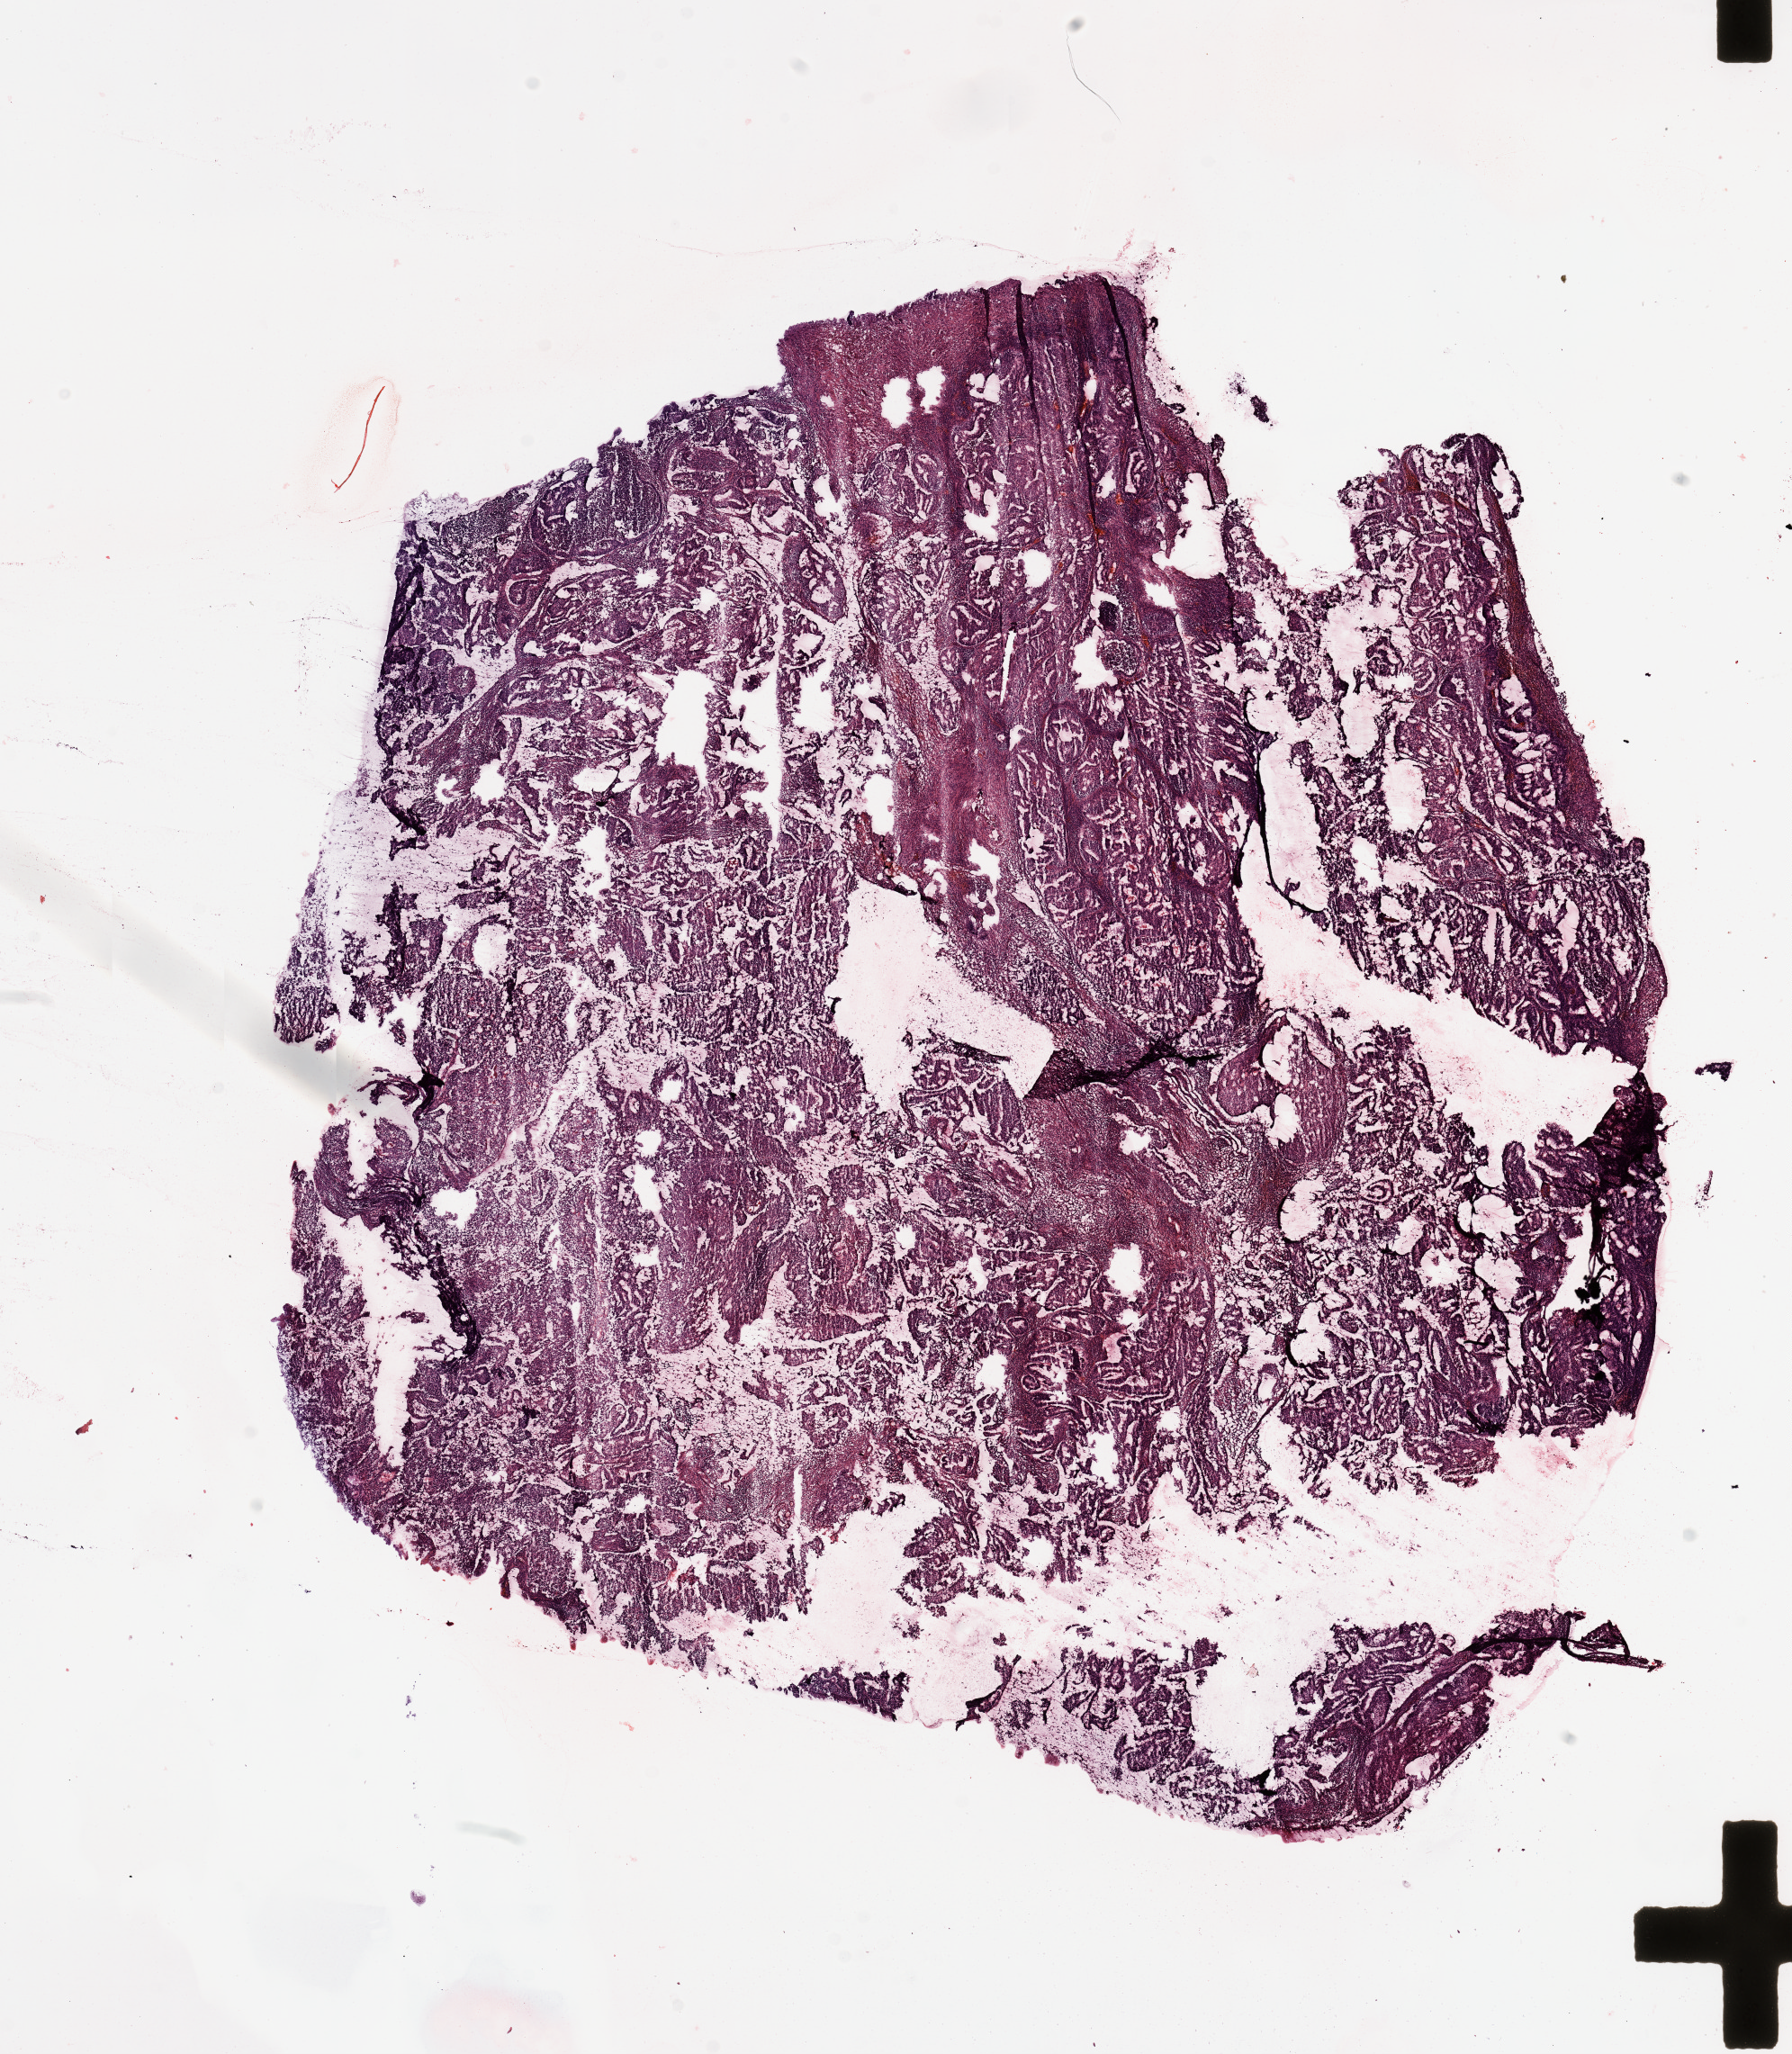
H&E-stained whole-slide image, a low-resolution overview of the entire scanned area, about 15.8 x 18.1 mm (slide scanned at 20x); uterus, tumour tissue. Female, 45 y/o. Histologic grade: G2 (moderately differentiated).
AJCC pathologic stage: I. Histologic diagnosis: Endometrioid adenocarcinoma, NOS.